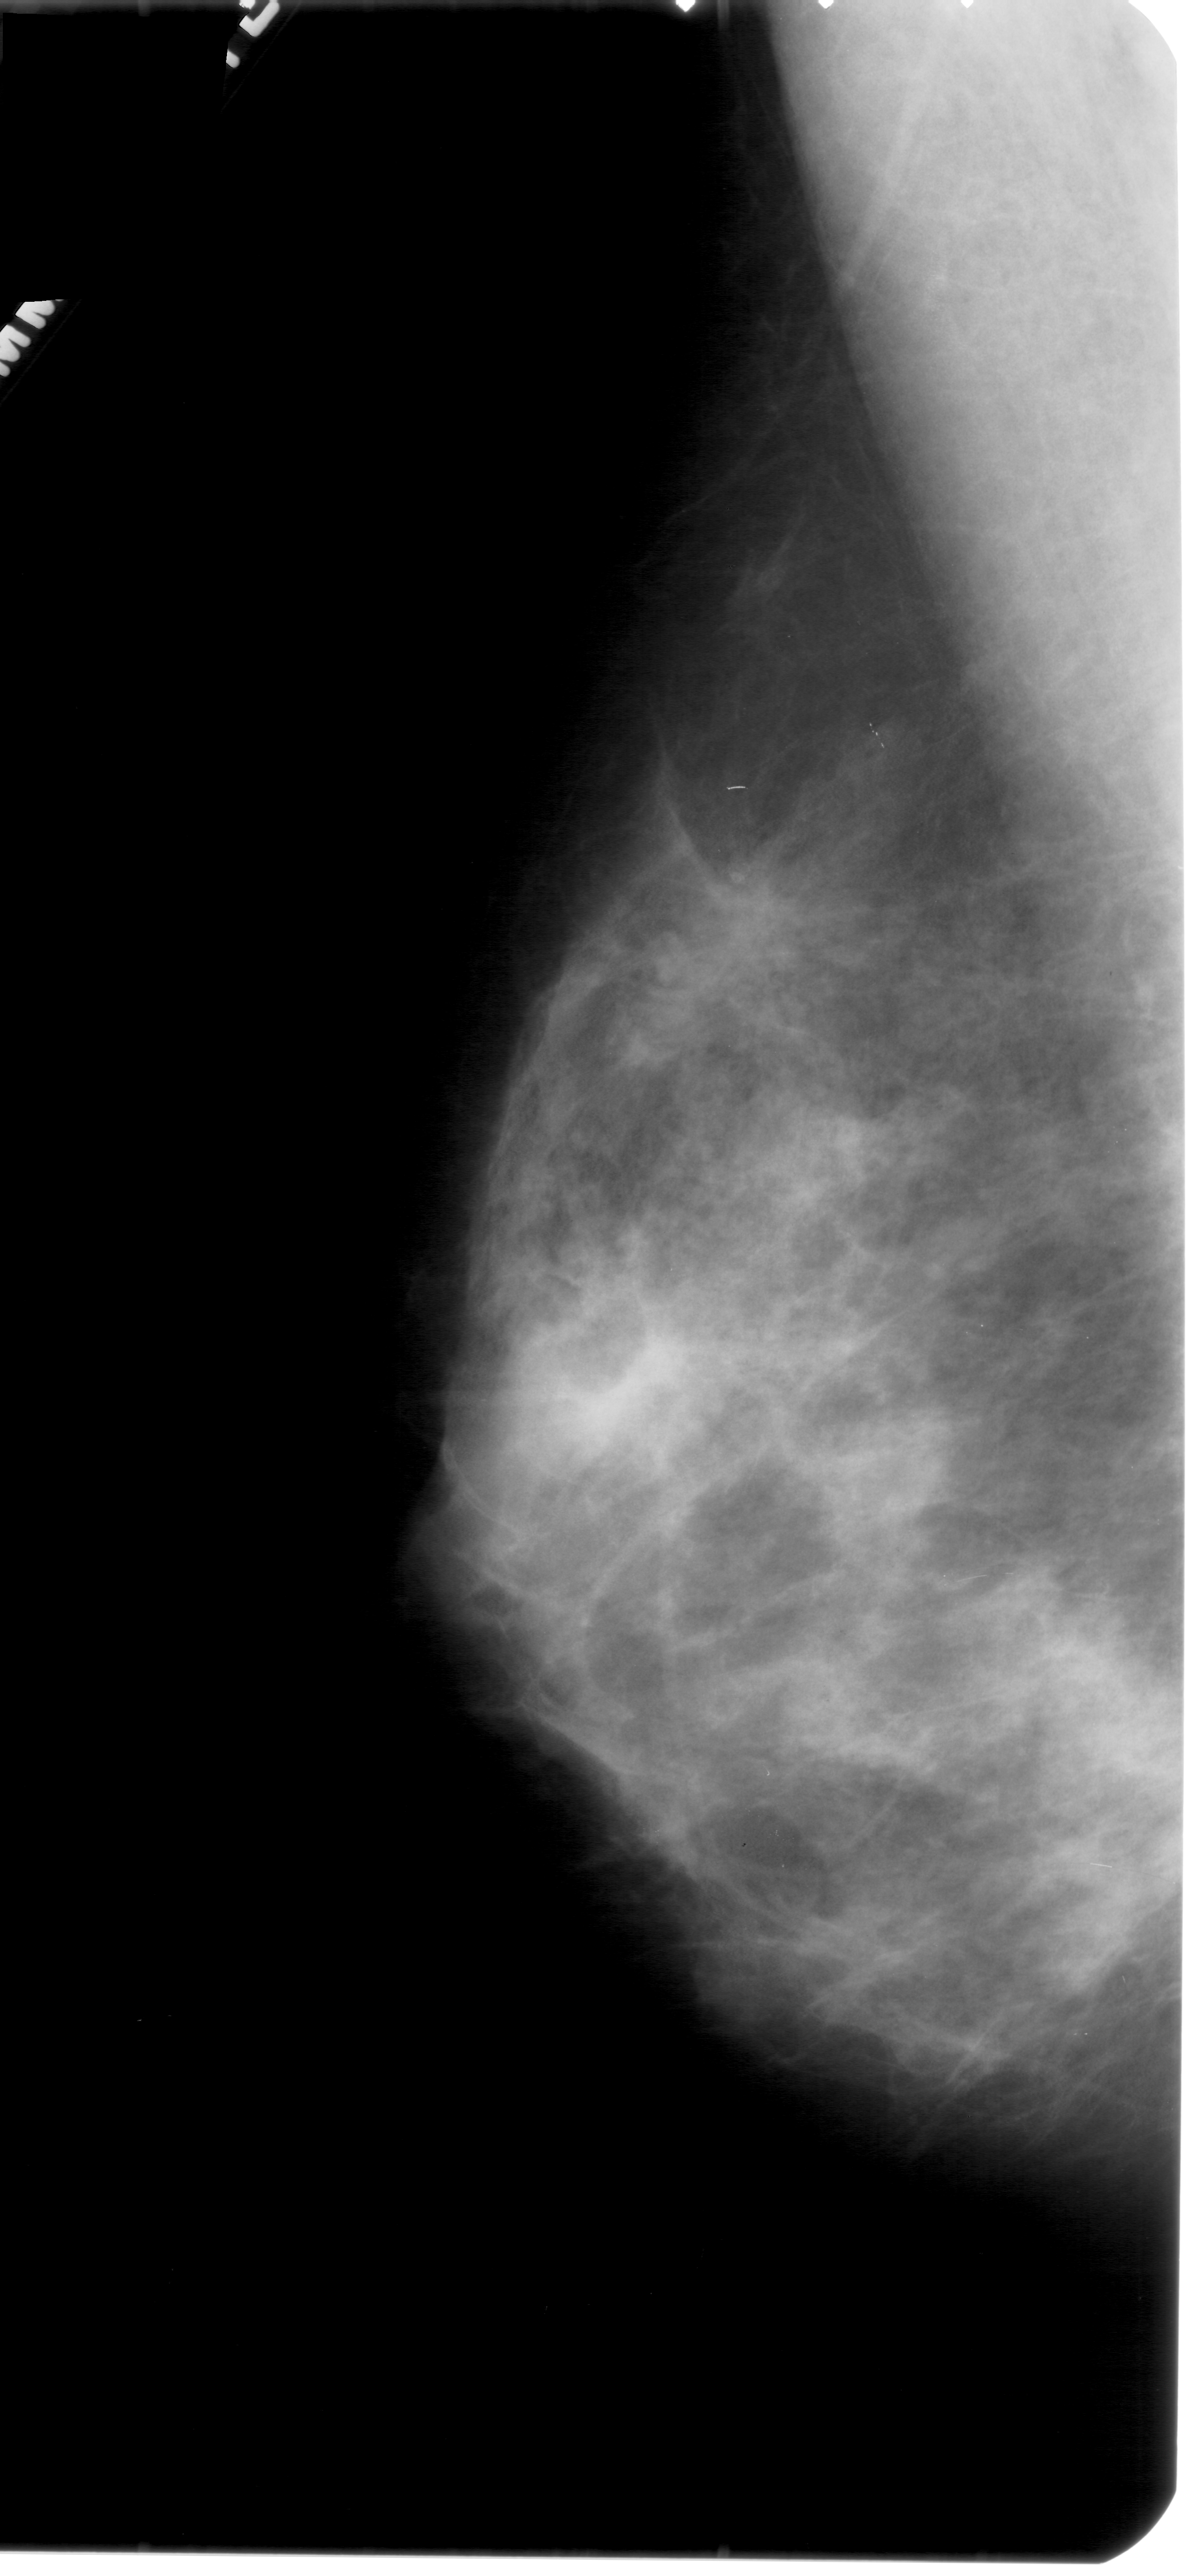
Mammogram (digitized film); left breast; mediolateral oblique (MLO) view; 1192 × 2576 image matrix.
Marked abnormalities (boxes around the expert regions of interest):
- mass, shape irregular, margins spiculated; BI-RADS assessment category 4; pathology (as recorded): malignant: bounding box [x1, y1, x2, y2] px = [687, 841, 817, 1010]